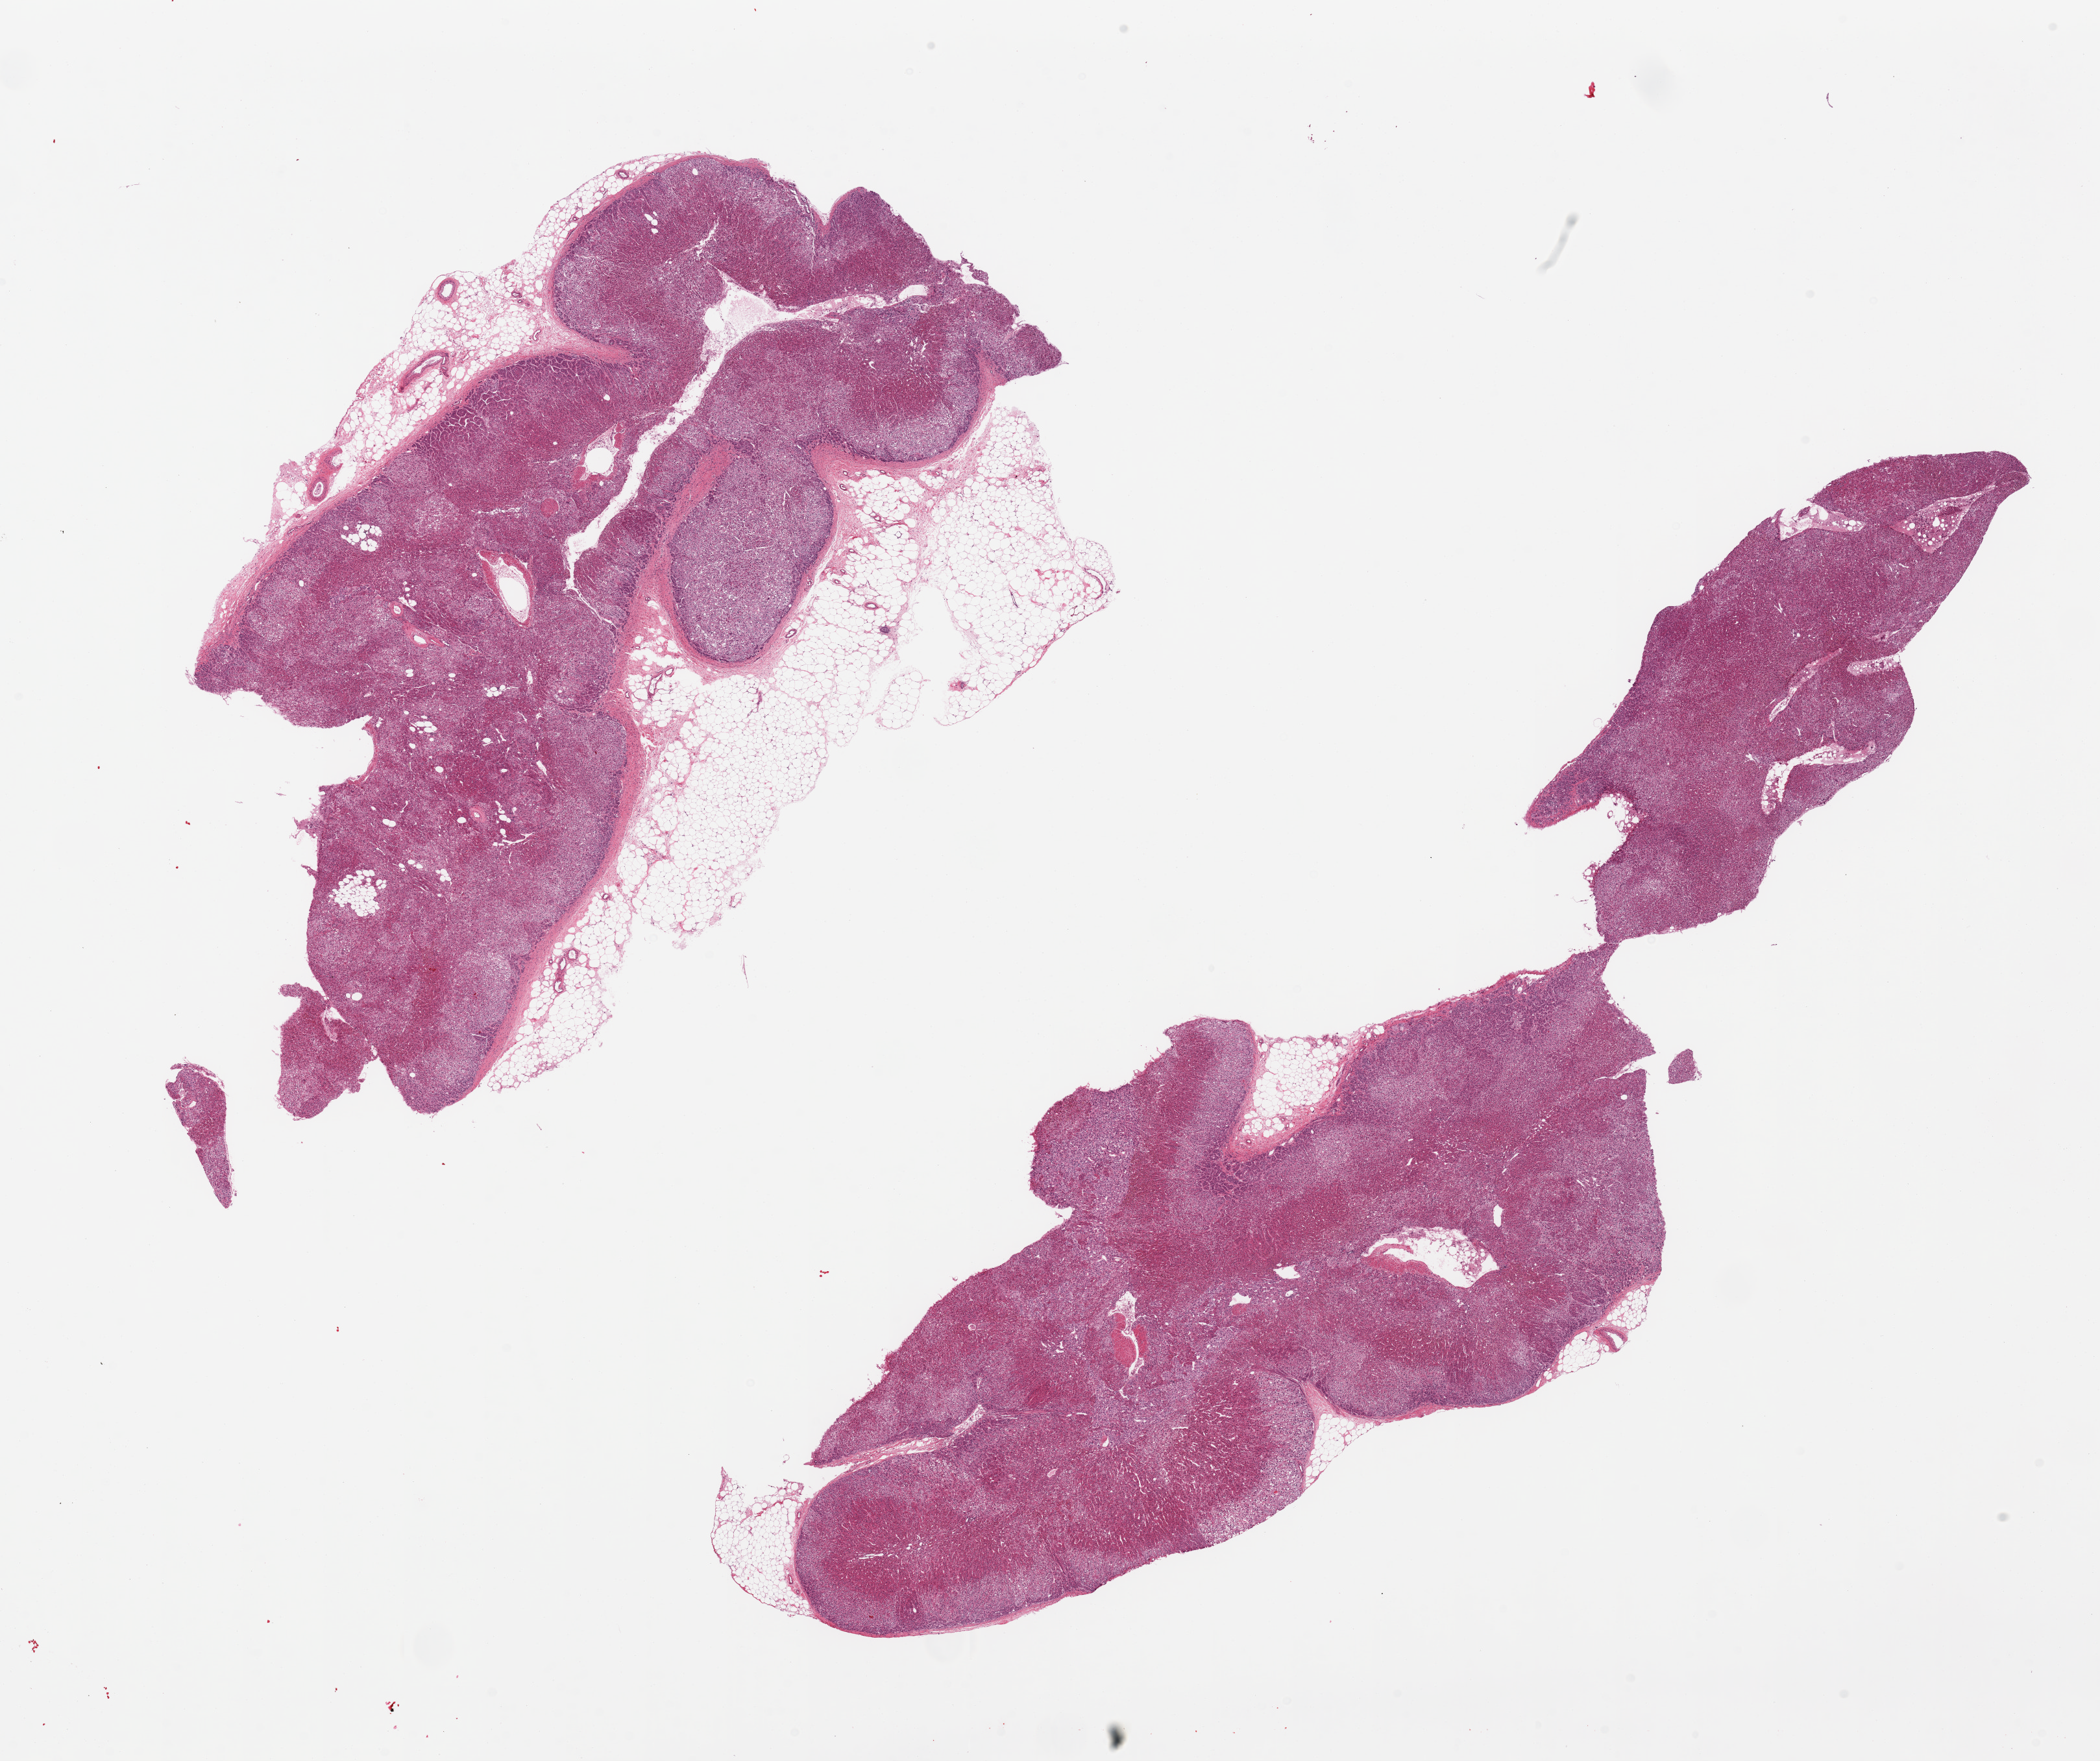
Haematoxylin and eosin whole-slide image — low-resolution overview of the scanned area, about 25.6 x 21.5 mm (acquisition: 20x scan), PAXgene-fixed, paraffin-embedded tissue, section of adrenal gland (target tissue), tissue donor sample. Donor: female.
Reviewer comment on this tissue sample: 2 pieces, one is ~30% adipose tissue.